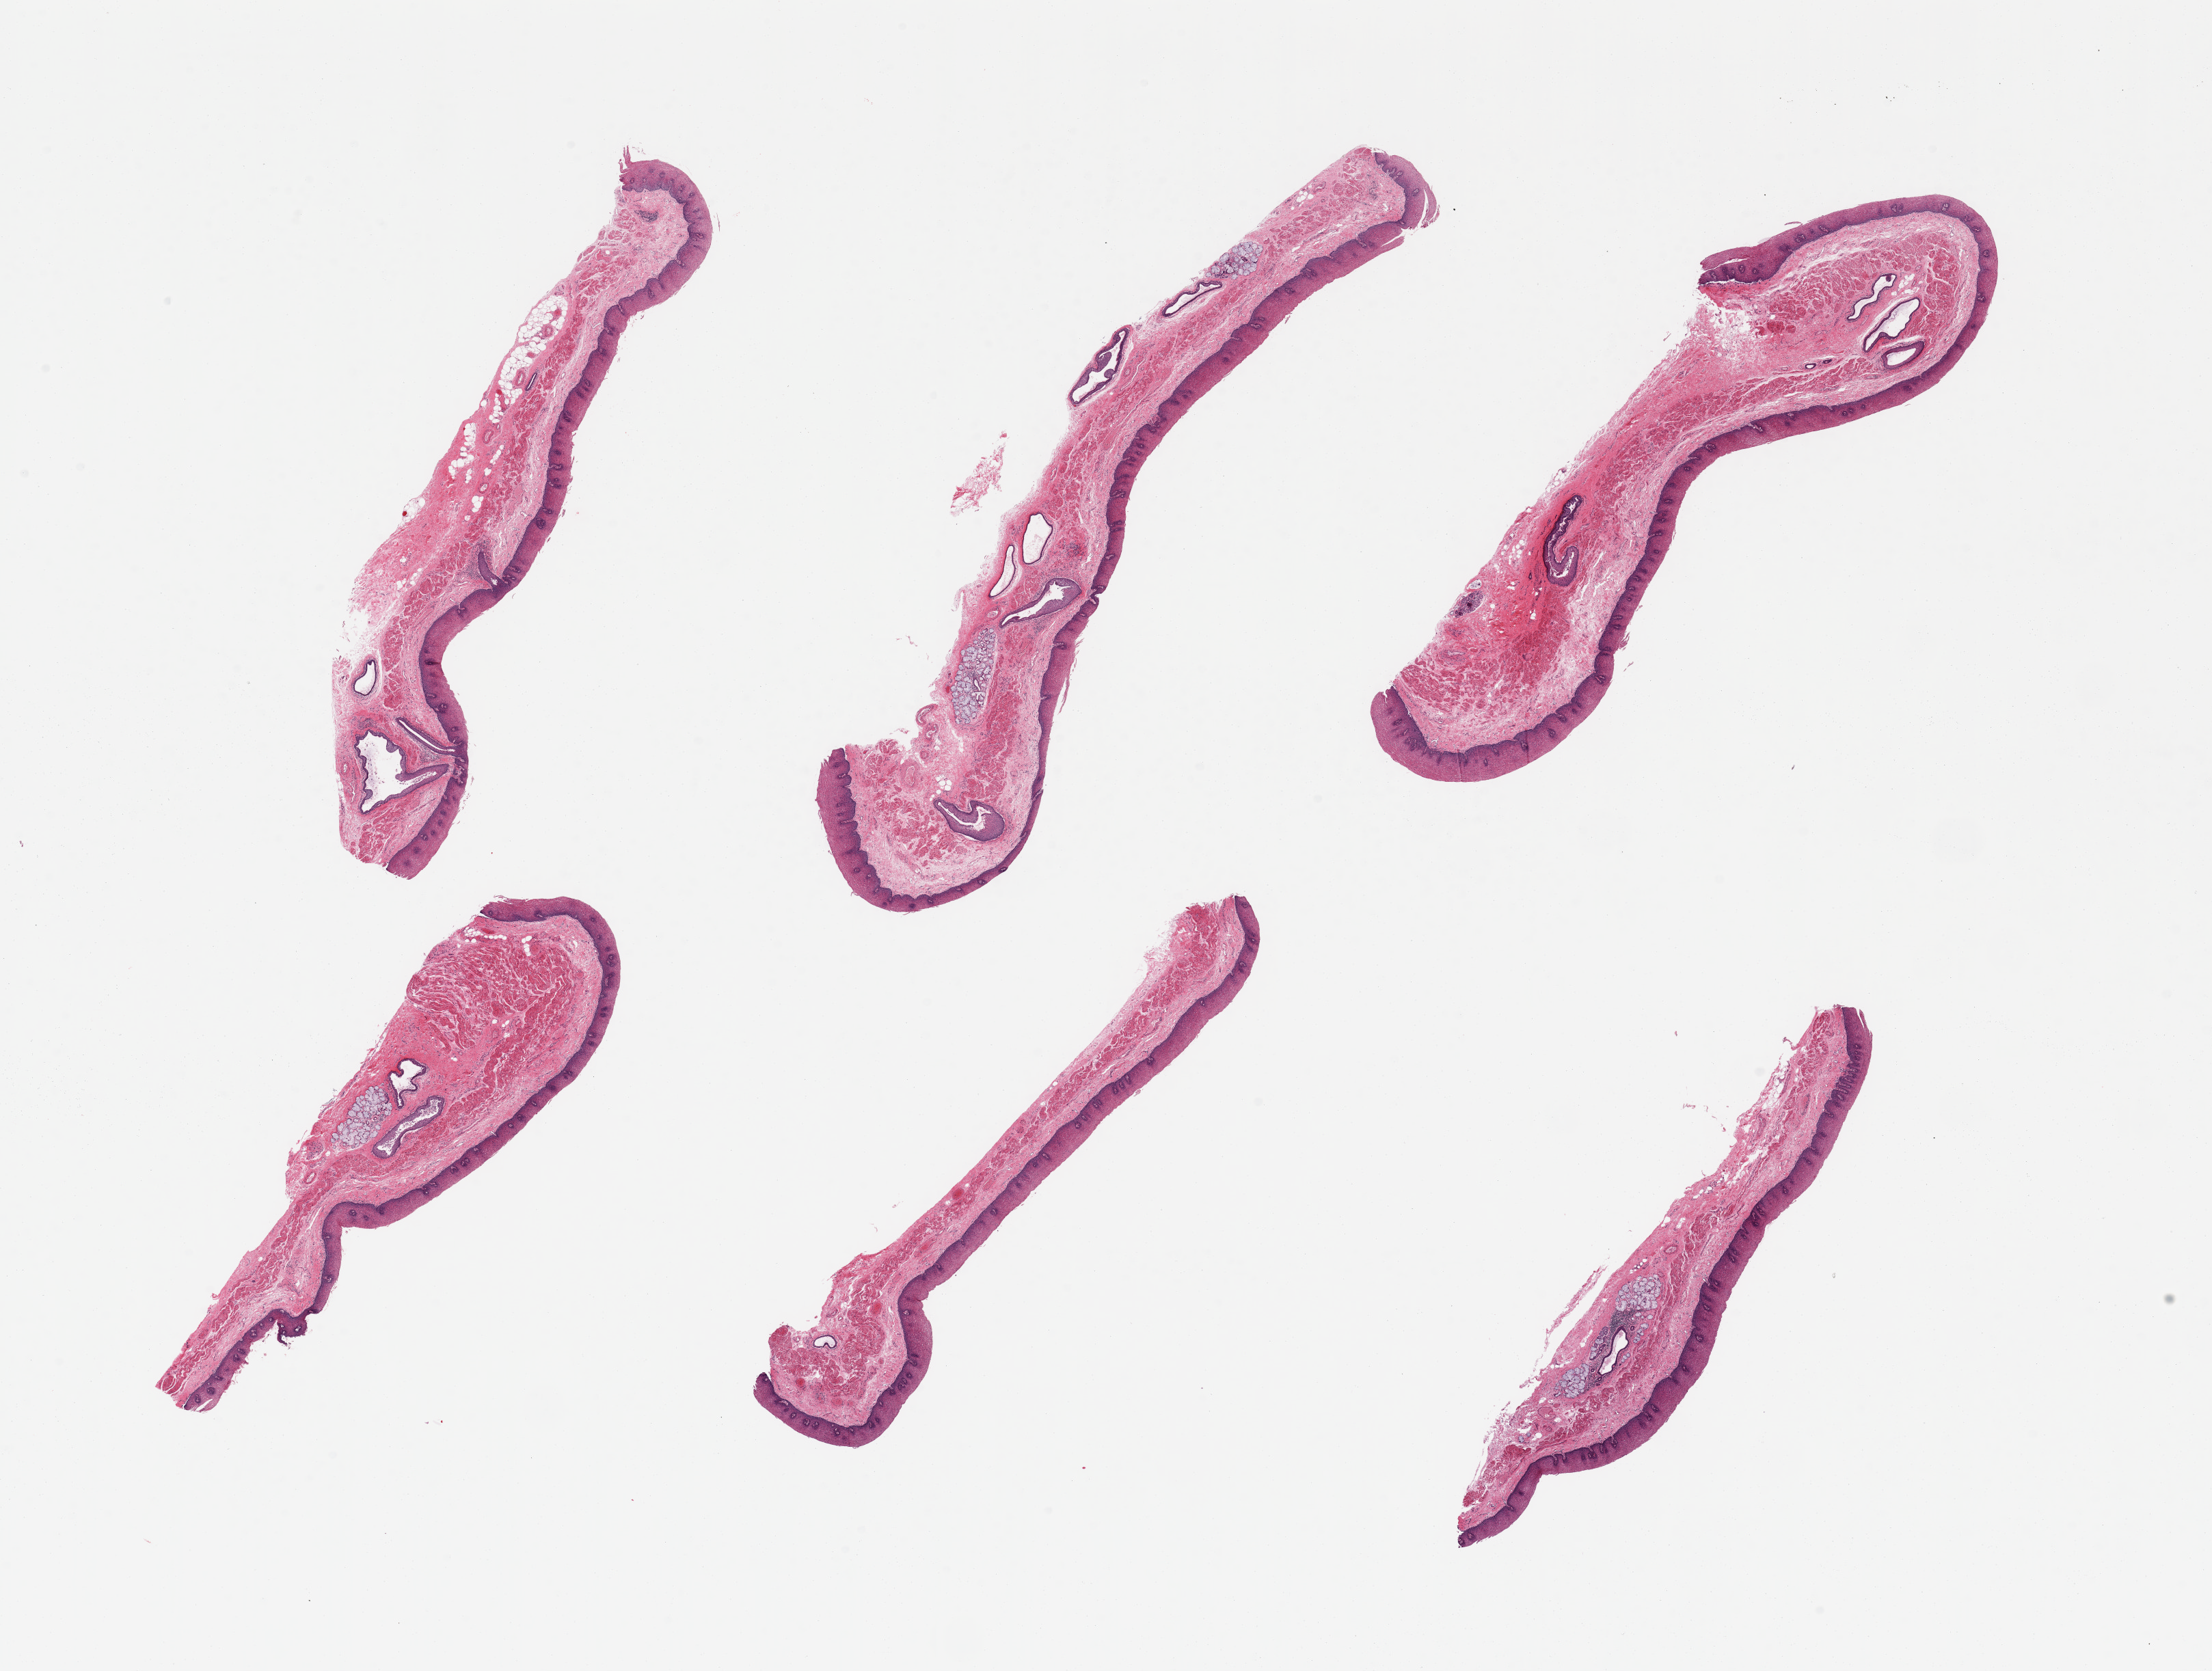
Whole-slide image, H&E stain — a low-resolution overview of the entire scanned area, about 25.6 x 19.3 mm, PAXgene-fixed, paraffin-embedded tissue, section of esophageal mucous membrane (target tissue), donor tissue sample. Donor sex: male.
Pathologist's review note for this sample: 6 pieces; ~0.2mm thick squamous epithelium; submucosal glands in 3 of 6 samples; well dissected.